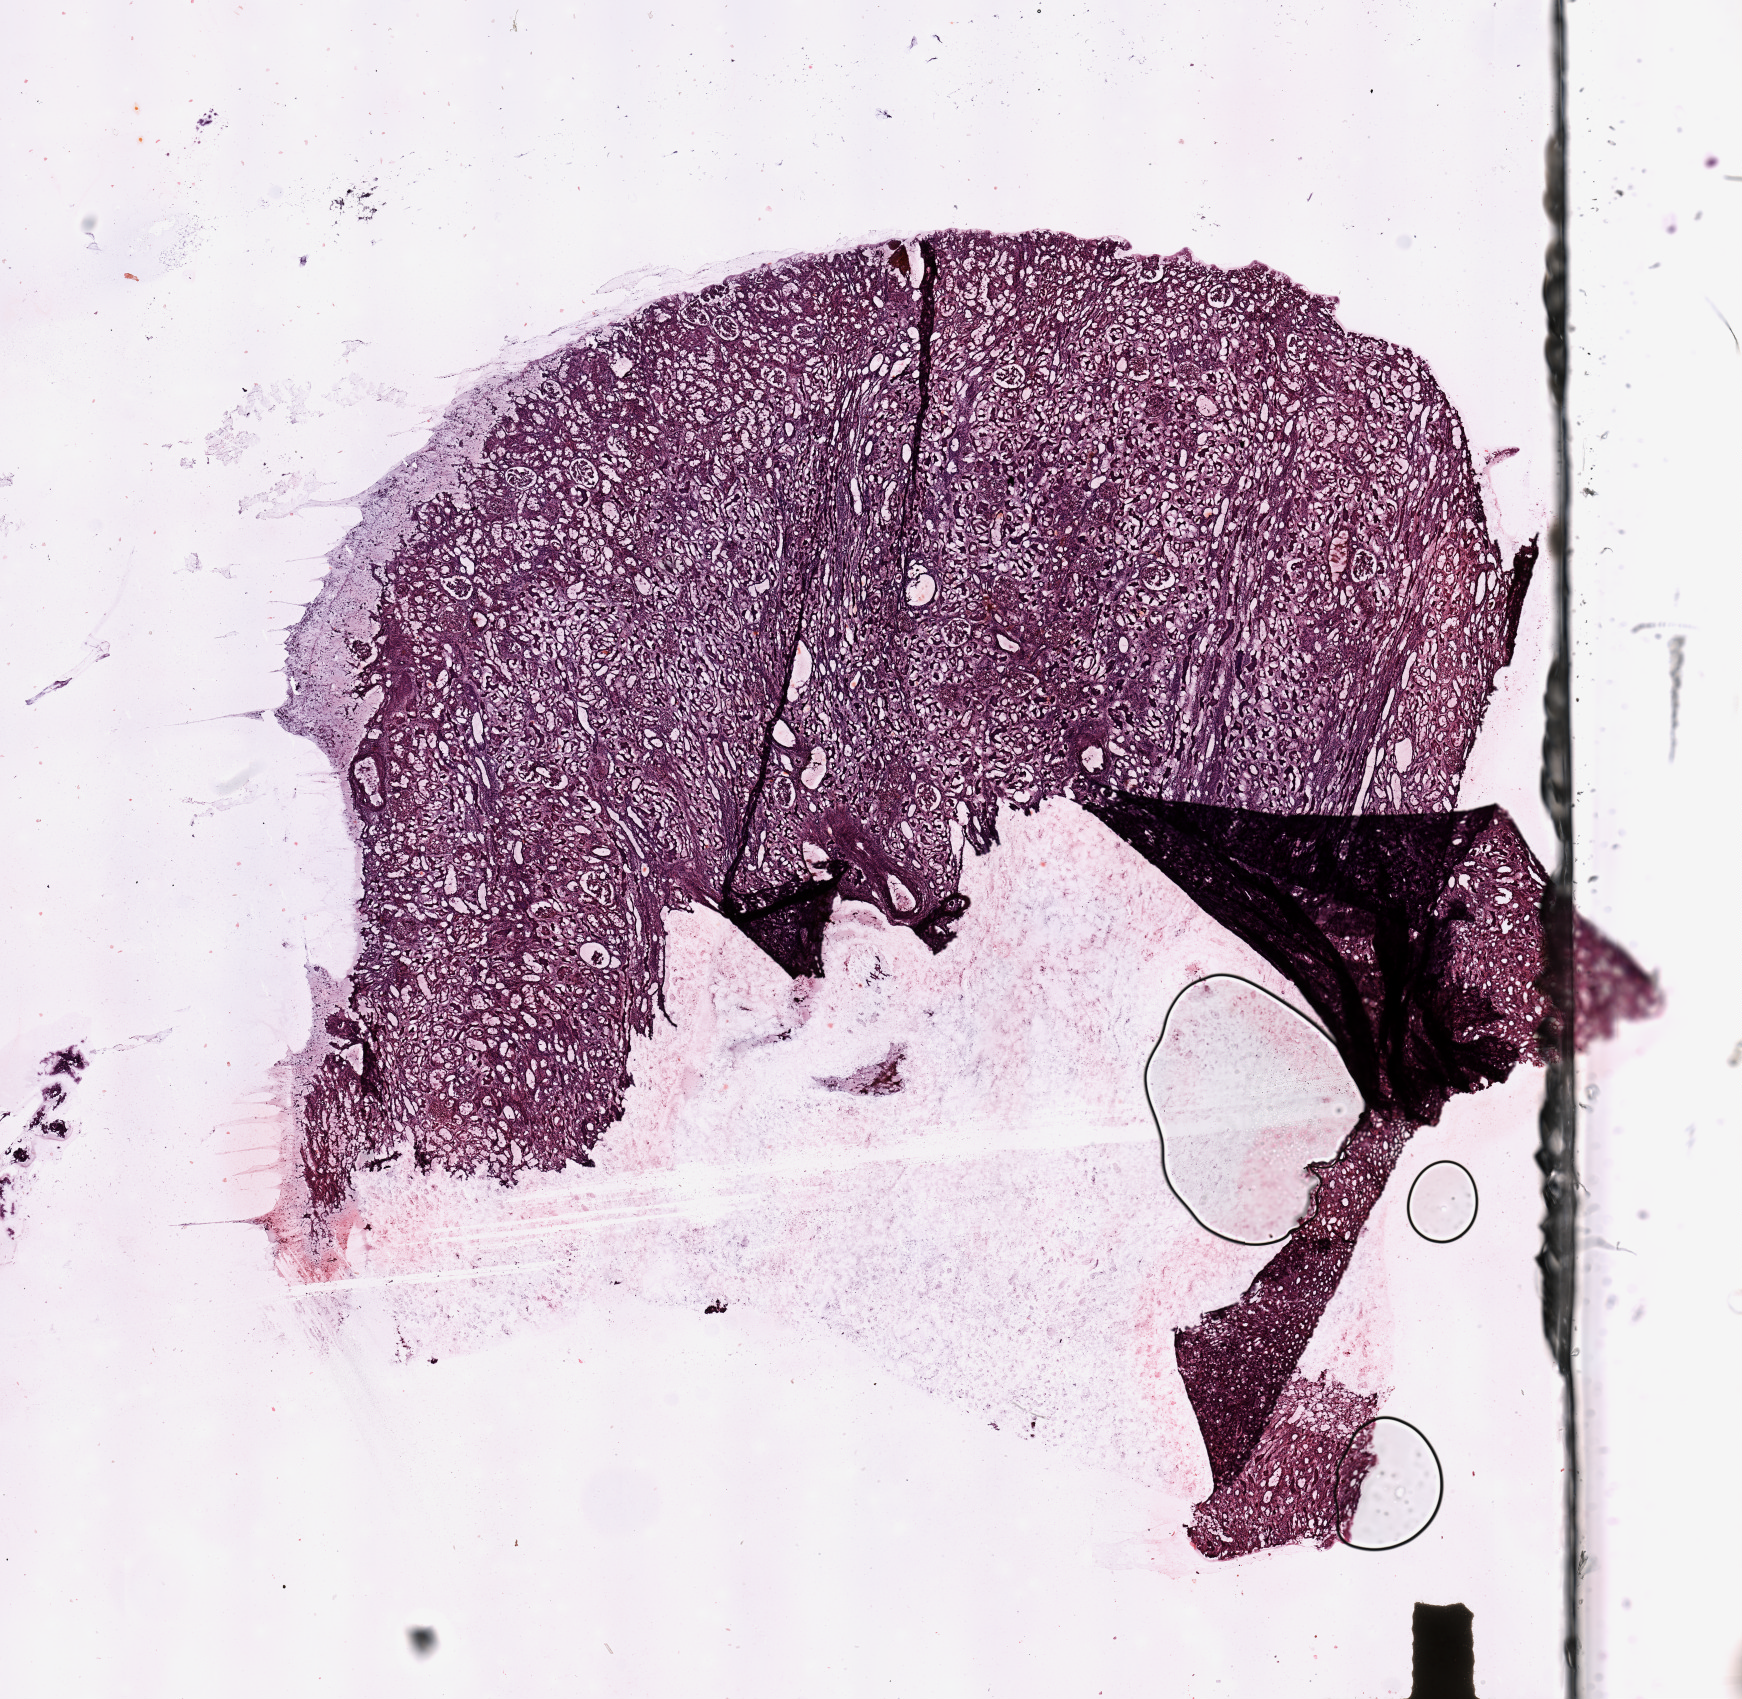
H&E-stained whole-slide image, a low-resolution overview of the entire scanned area, about 13.8 x 13.4 mm (slide scanned at 20x), kidney, normal (non-tumour) tissue. 58-year-old male patient.
This section: normal (non-tumour) tissue from the same patient. Patient diagnosis: Renal cell carcinoma, NOS.